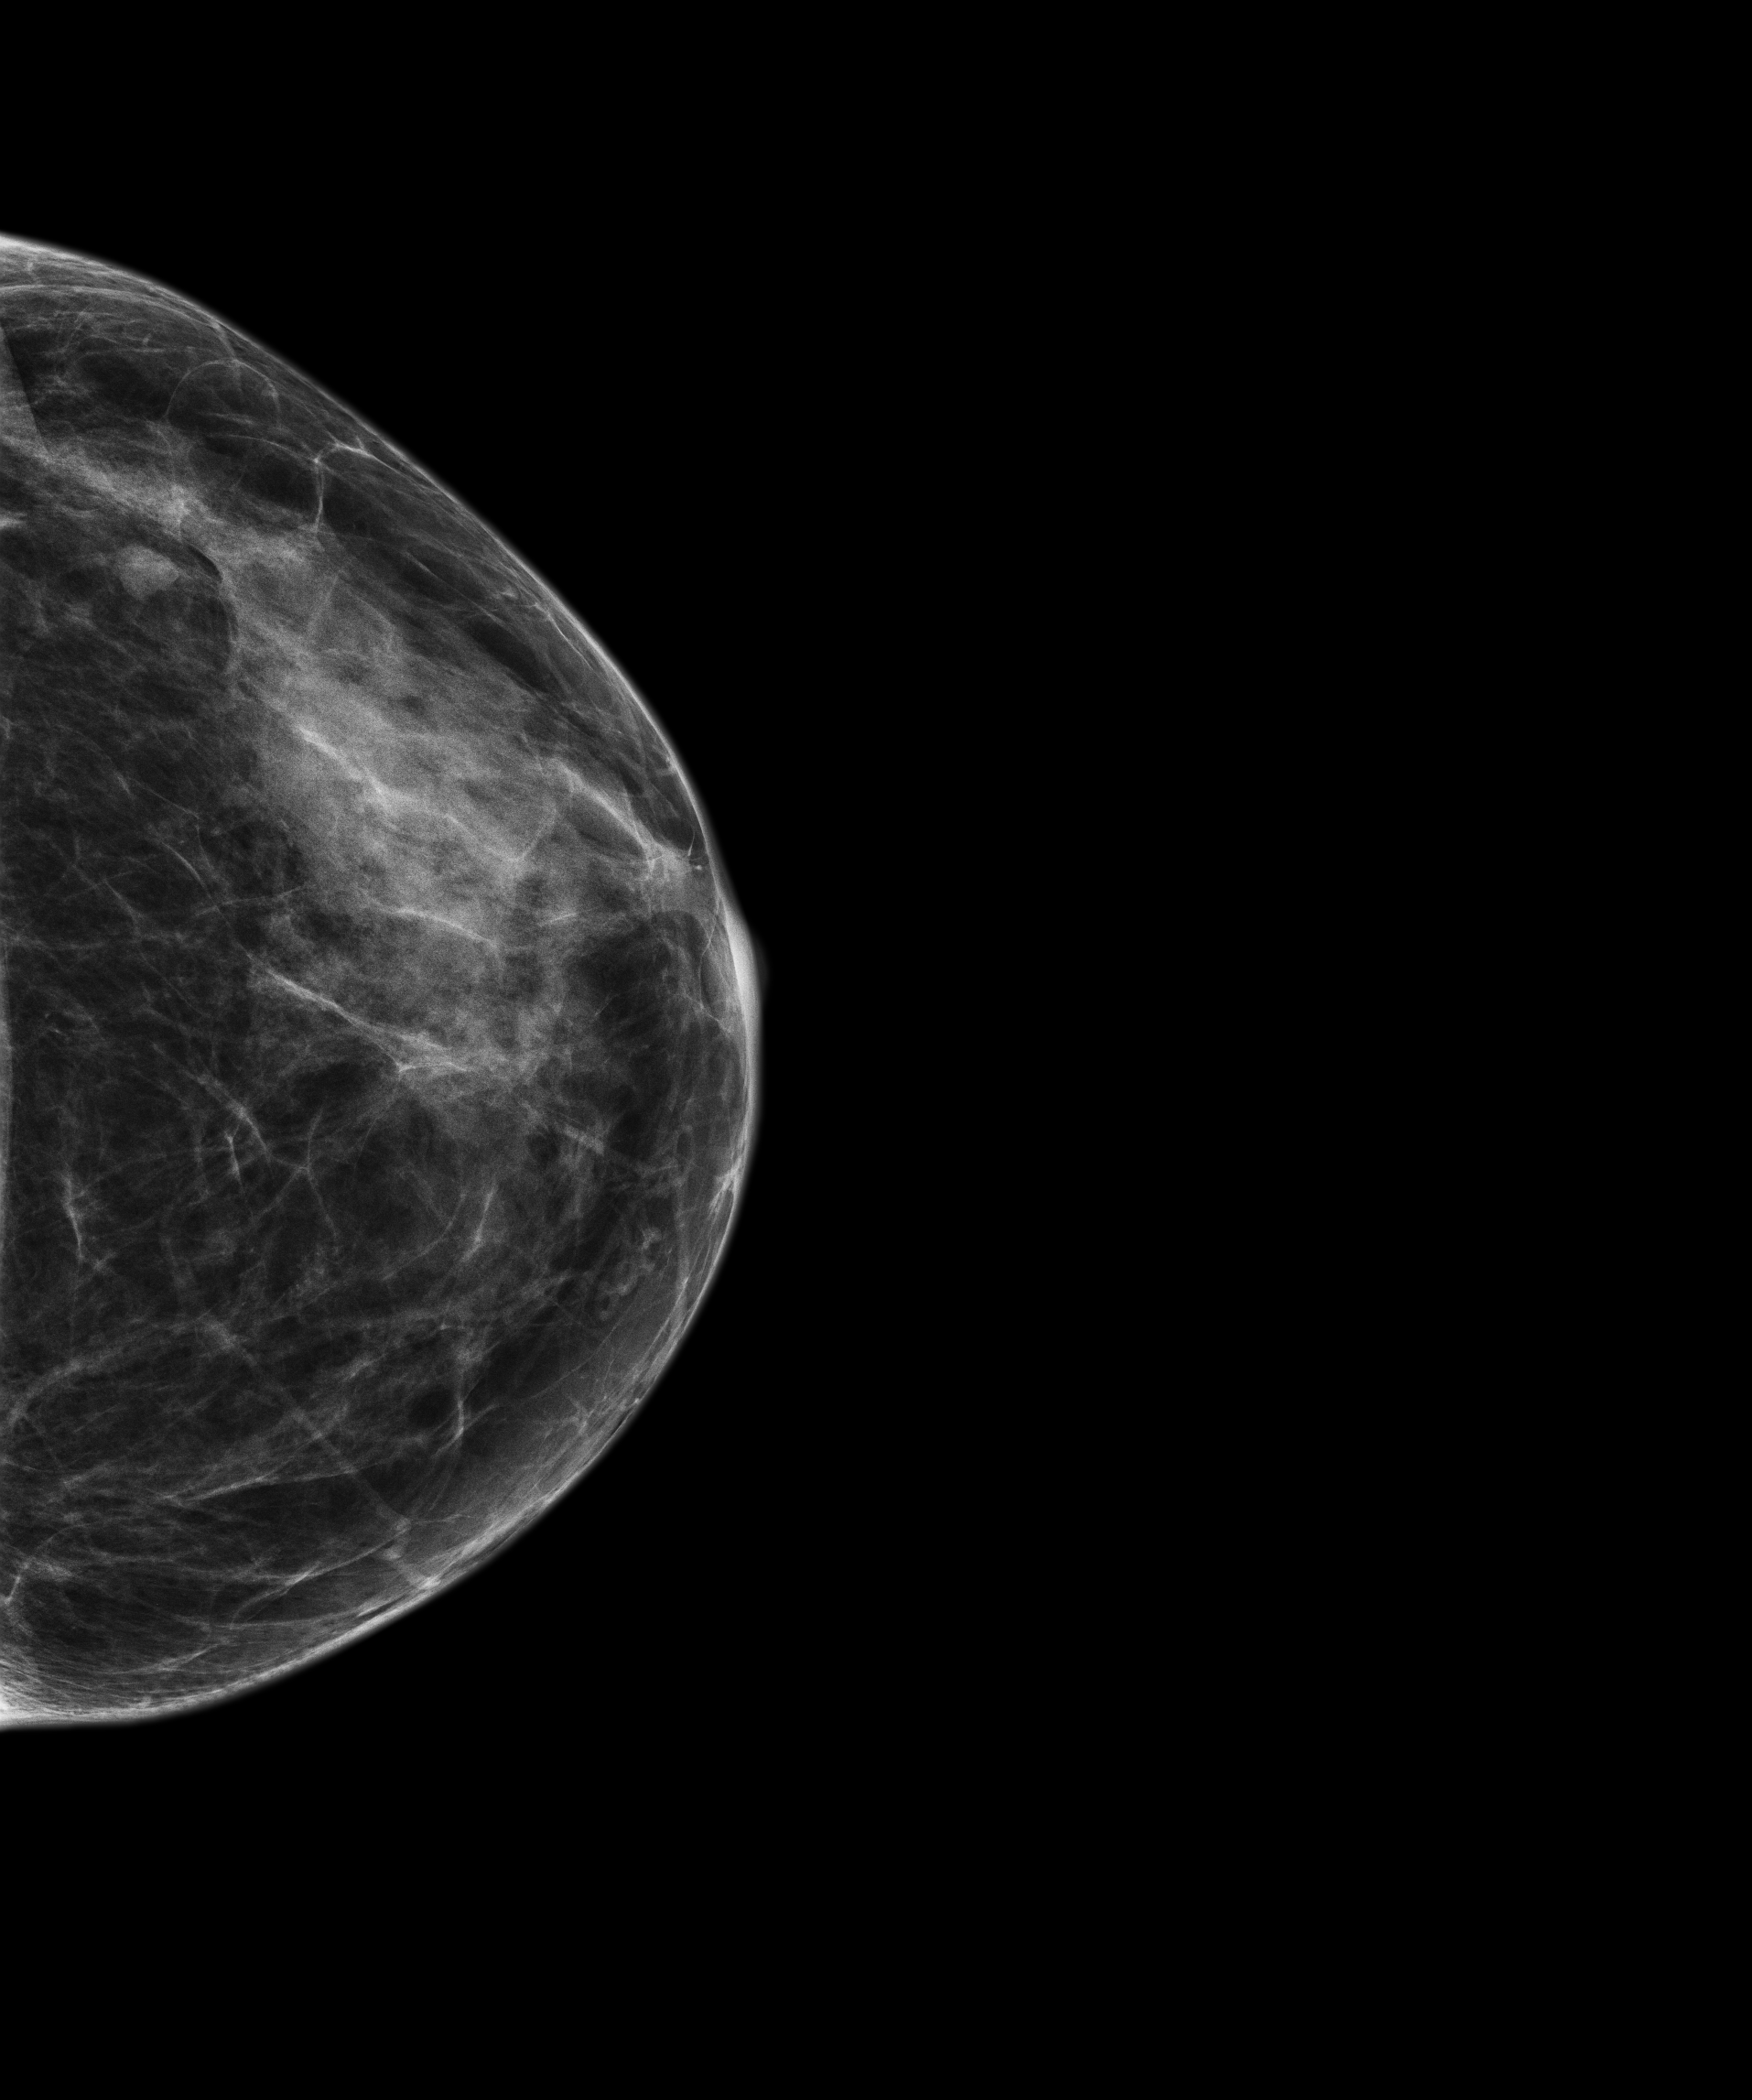
Screening examination, compressed breast thickness 33 mm. Female patient, age 48 years.
Image type: full-field digital mammogram. Breast: left. Projection: cranio-caudal projection.